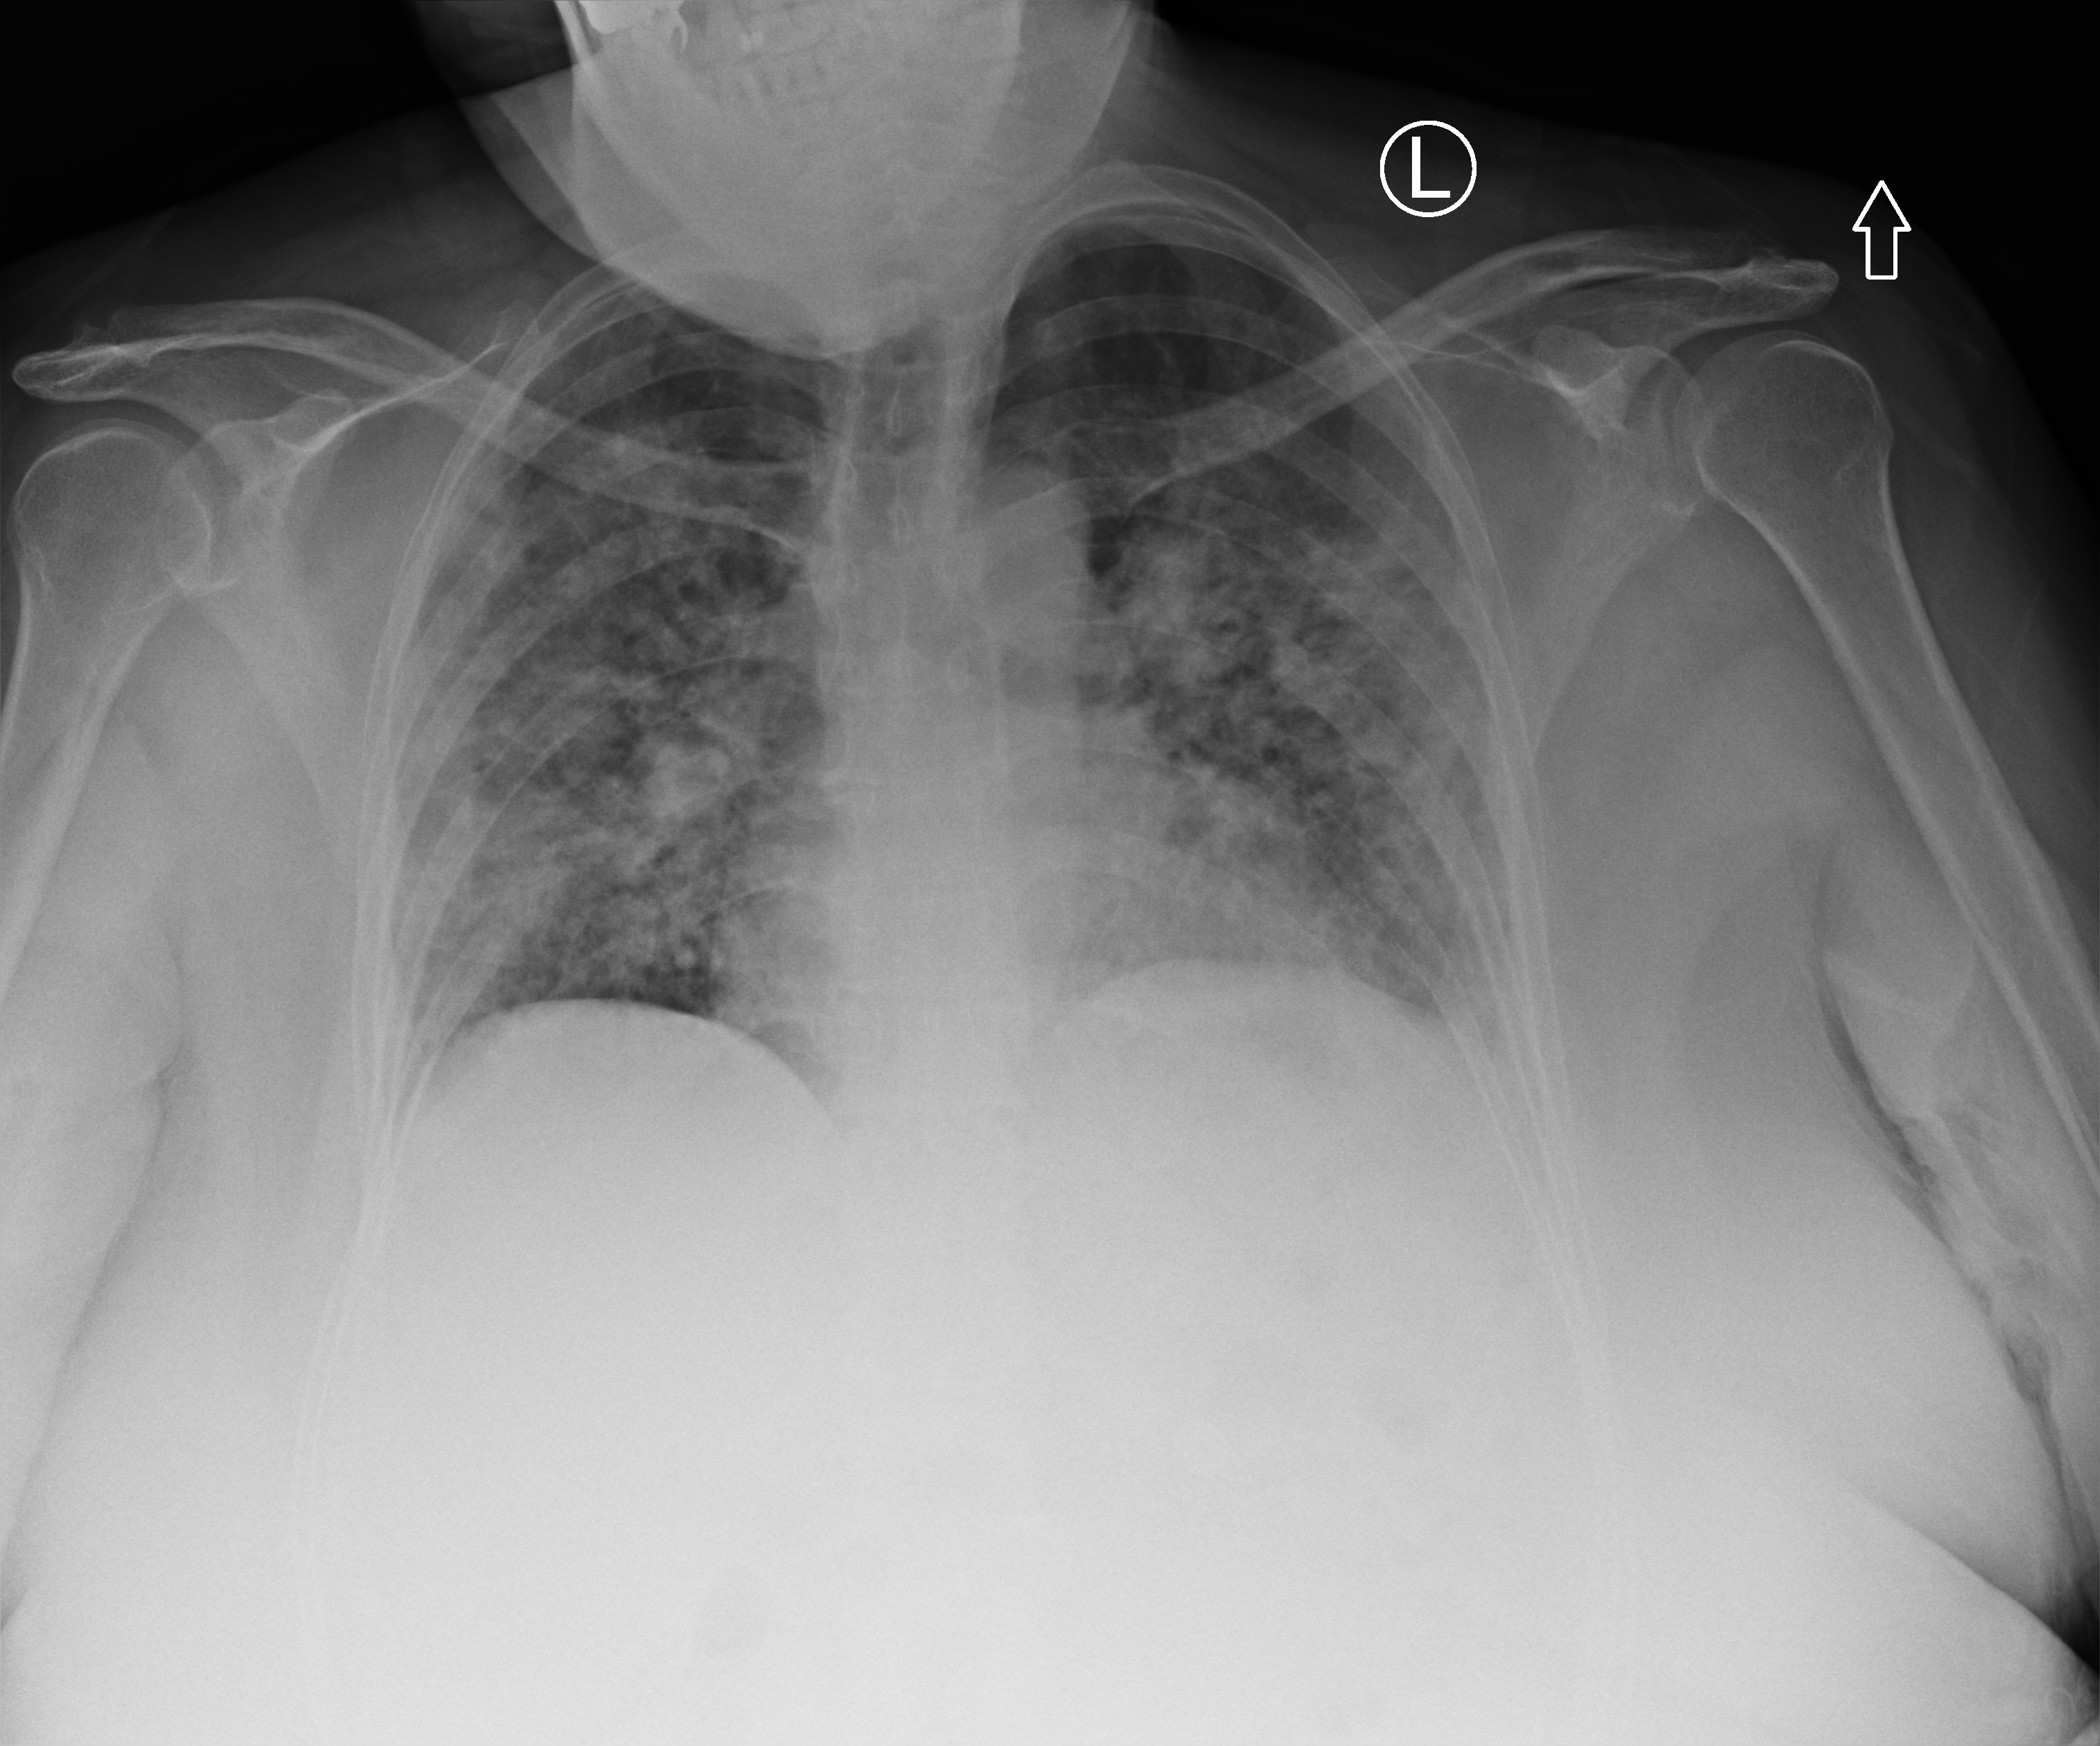
Bedside chest radiograph (computed radiography), anteroposterior (AP) projection. Patient hospitalised with COVID-19; female, aged 18–59 years.
Hospital-stay facts (about this admission, not read from this image; timing relative to this image not recorded):
- mechanically ventilated during this hospital stay: no